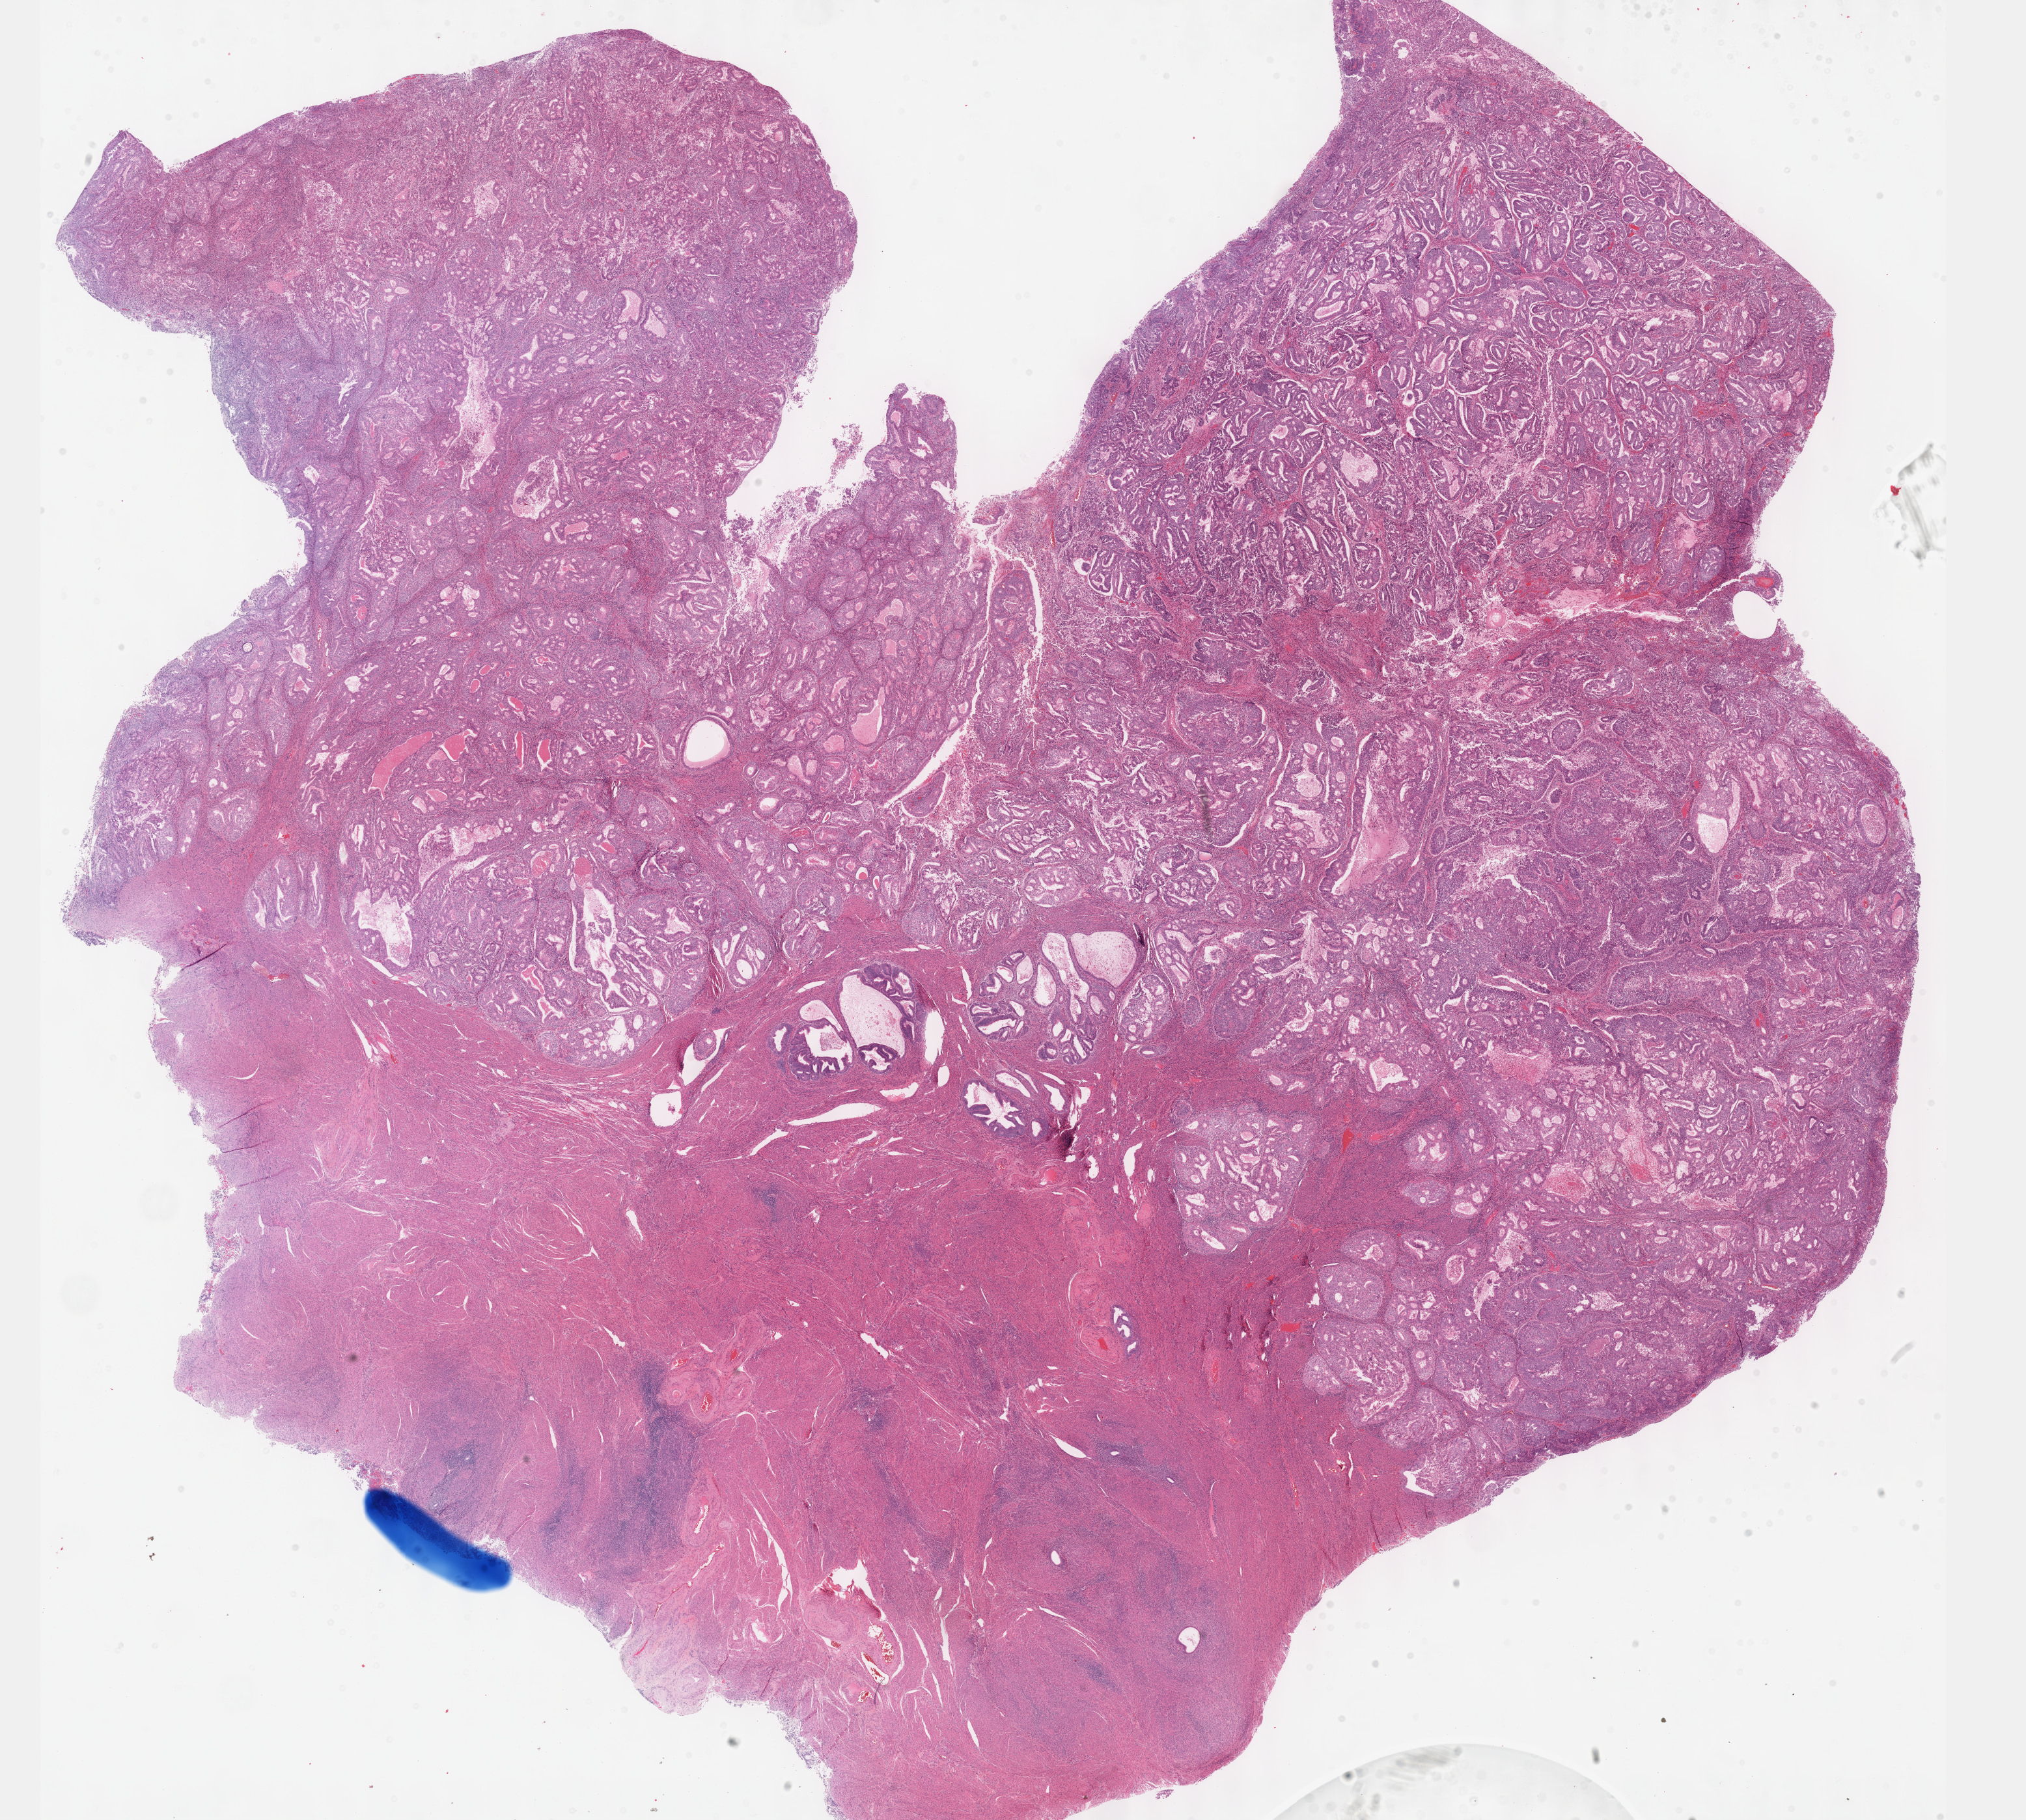
Digitized Hematoxylin and eosin (H&E) stained tissue section (whole slide) — a low-resolution overview of the entire scanned area, about 25.1 x 22.6 mm; formalin-fixed paraffin-embedded (FFPE) diagnostic section; primary tumour sample from the uterus. Female patient; age at initial diagnosis 70 years. Histologic grade: G2 (moderately differentiated).
FIGO stage: I. Histologic diagnosis: Endometrioid adenocarcinoma, NOS.